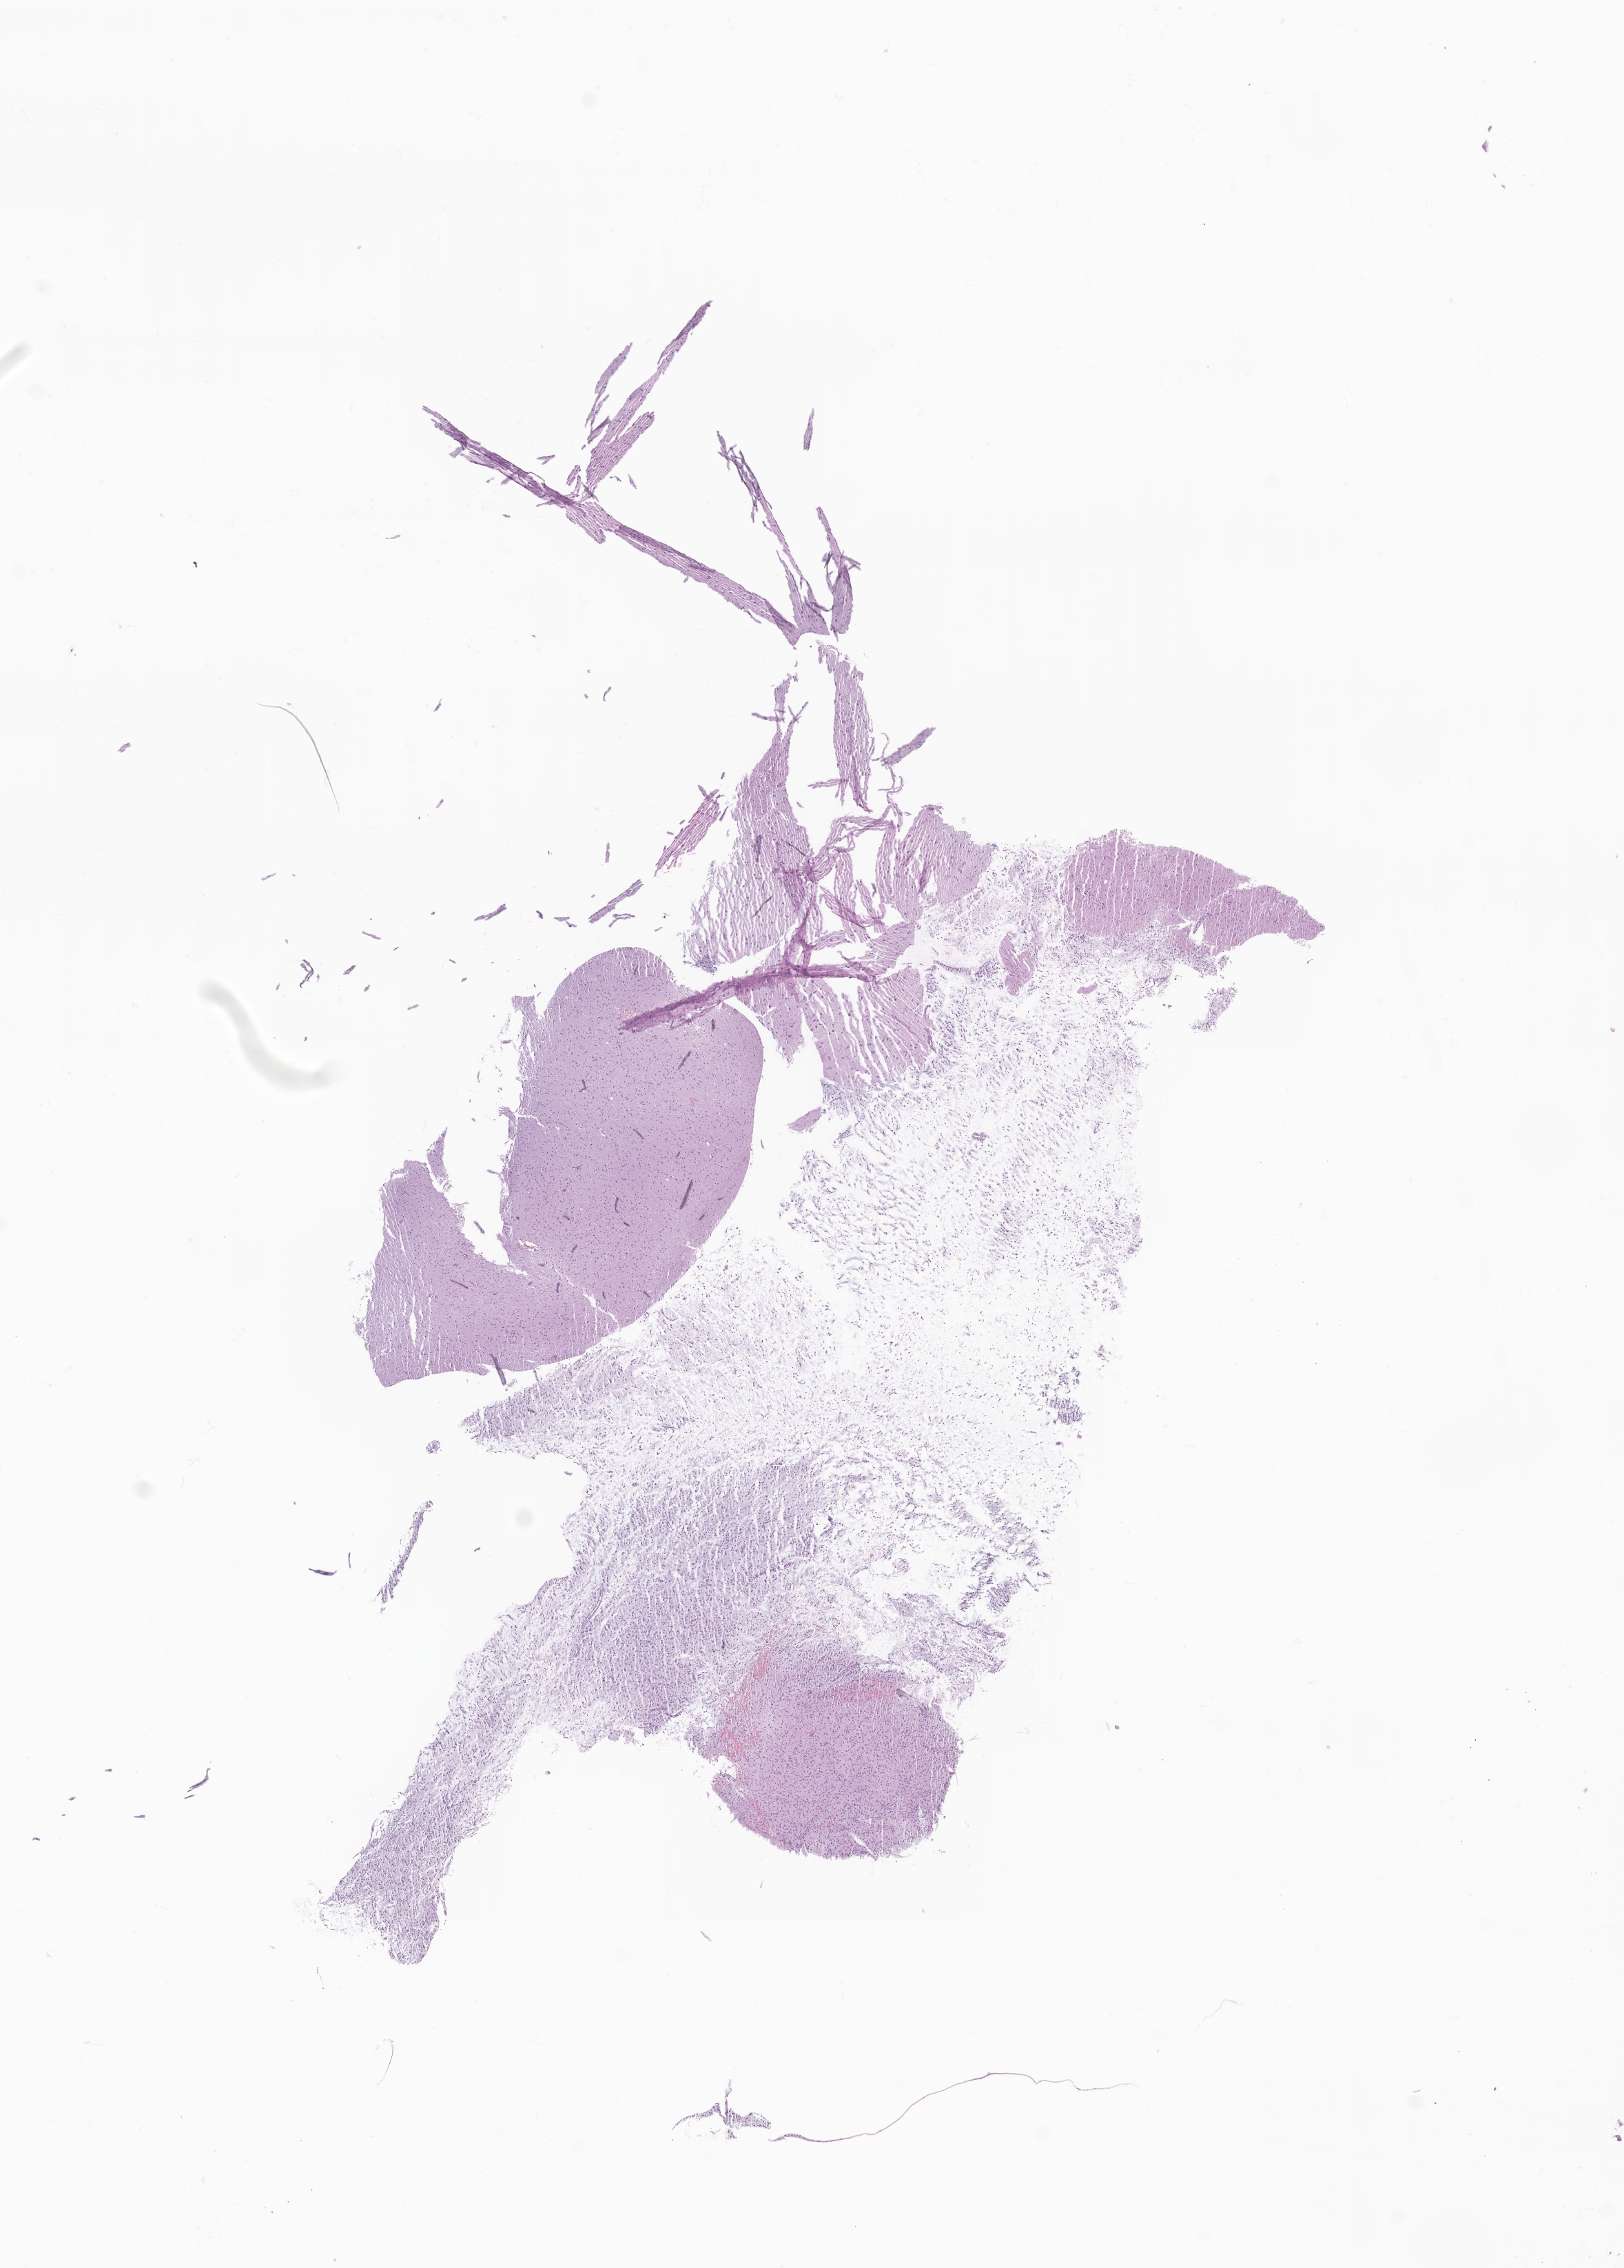
Haematoxylin and eosin whole-slide image of tumor tissue from the brain, a low-resolution overview of the entire scanned area, about 9.9 x 13.9 mm, formalin-fixed, paraffin-embedded (FFPE) tissue. Patient: male, age 219 months (18 years 3 months).
Diagnosis (ICD-O-3 morphology term): Dysembryoplastic neuroepithelial tumor.